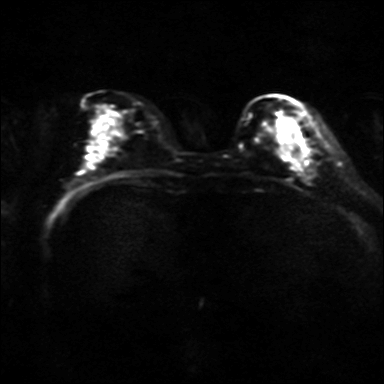
Breast MRI, one axial slice. Slice 14 of 36 in the series (ordered by position). Diffusion-weighted series; image 2 of 4 stored at this slice position (different b-values; order by instance number). 3 T. 4 mm slice thickness. 384 × 384 image matrix, field of view 320 × 320 mm. Female patient.
Structures marked on this image (expert manual segmentation):
- tumour on diffusion-weighted imaging: bounding box [x1, y1, x2, y2] px = [289, 150, 300, 167]